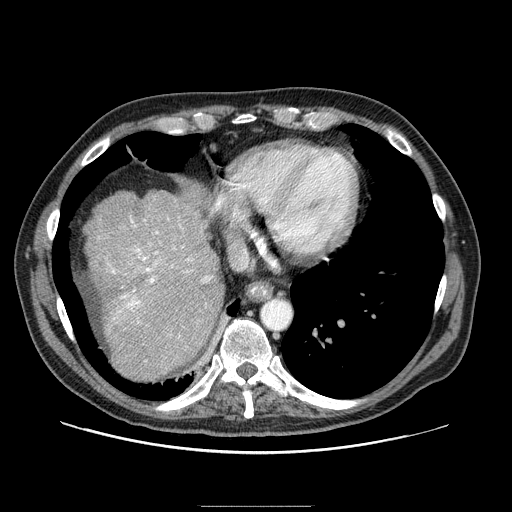
Contrast-enhanced abdominal CT (liver protocol), one axial slice; slice 77 of 99 in the series (ordered by position); reconstruction kernel STANDARD; 100 kVp; one of 2 acquisitions stored at this slice position; soft-tissue window (W 400 / L 40 HU); 512 × 512 image matrix, field of view 400 × 400 mm. From the clinical record (not read from this slice): diagnosis: hepatocellular carcinoma (patient treated with transarterial chemoembolisation; whether this scan precedes or follows treatment is not stated here); TNM stage (as recorded): Stage-II; Child-Pugh class: A; tumour differentiation: well differentiated; tumour nodularity: multinodular.
Structures marked on this image (semi-automatic segmentation, software-assisted and operator-edited):
- liver parenchyma outside the tumour (the mass and vessels are separate outlines, so this box may not span the whole liver): bounding box [x1, y1, x2, y2] px = [88, 188, 224, 378]
- liver vessels: [108, 219, 212, 324]